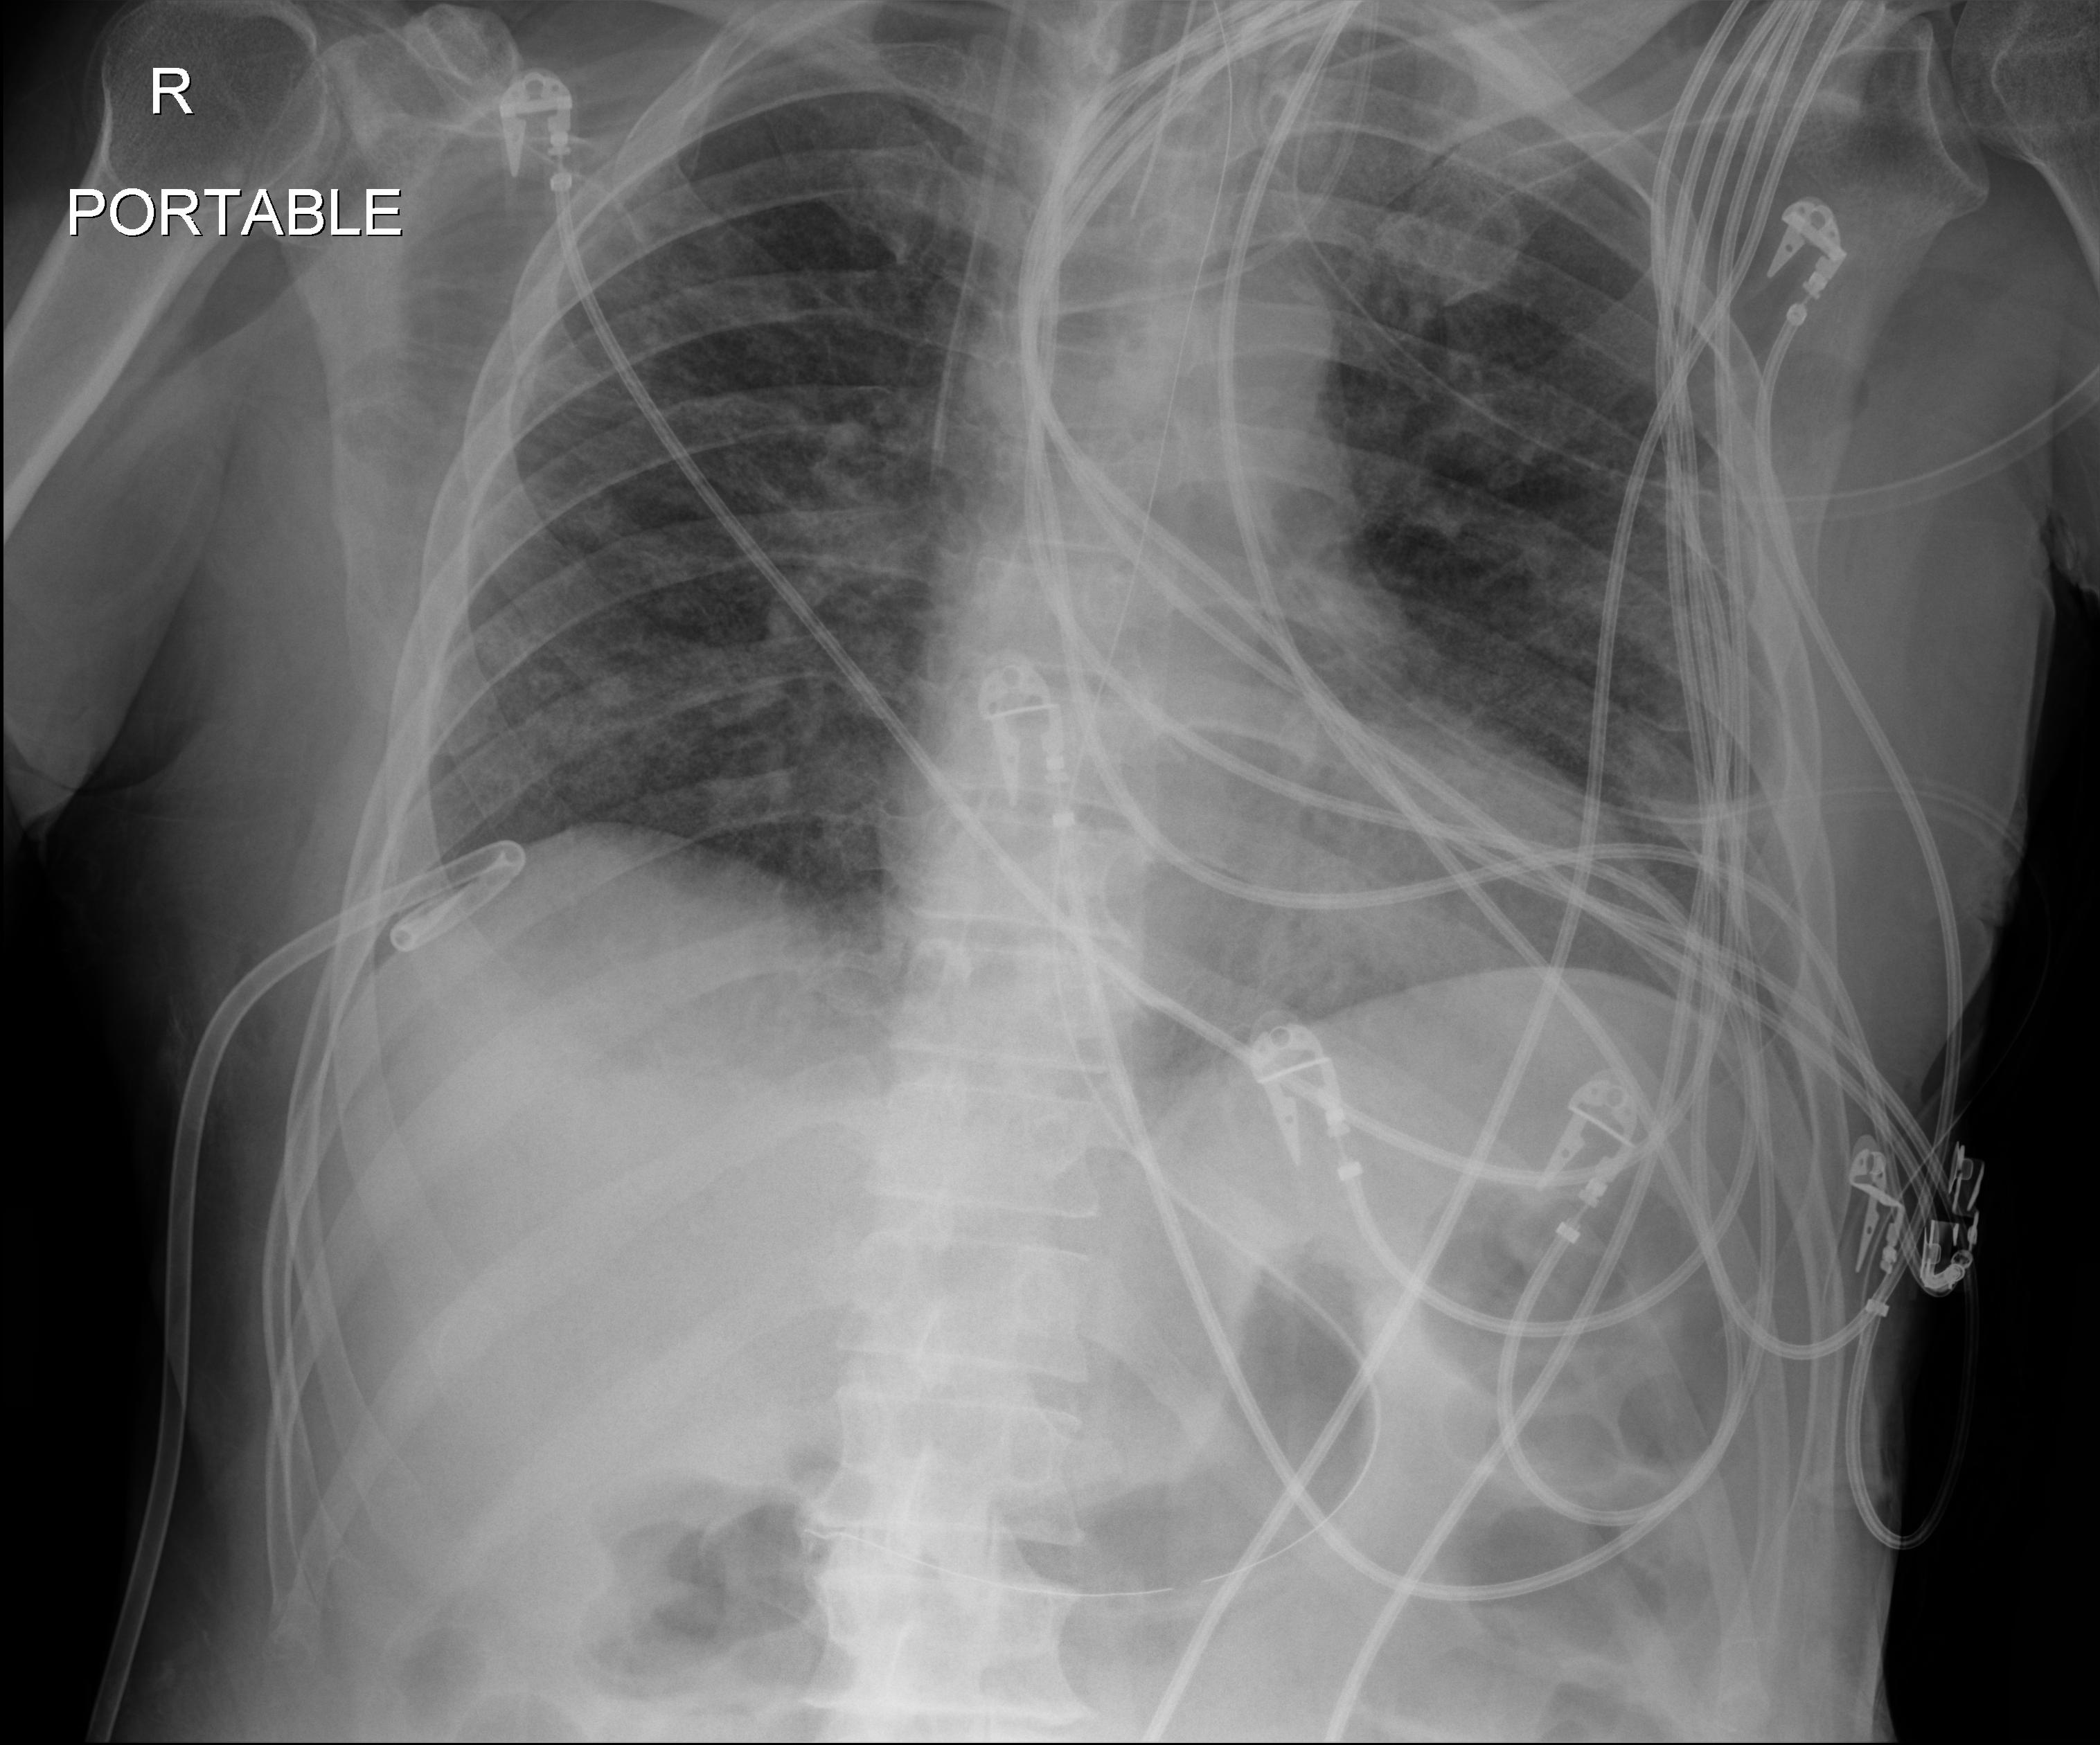
Chest X-ray (portable), anteroposterior (AP) projection. Patient hospitalised with COVID-19; male, aged 18–59 years.
Hospital-stay facts (about this admission, not read from this image; timing relative to this image not recorded): mechanically ventilated during this hospital stay: yes.